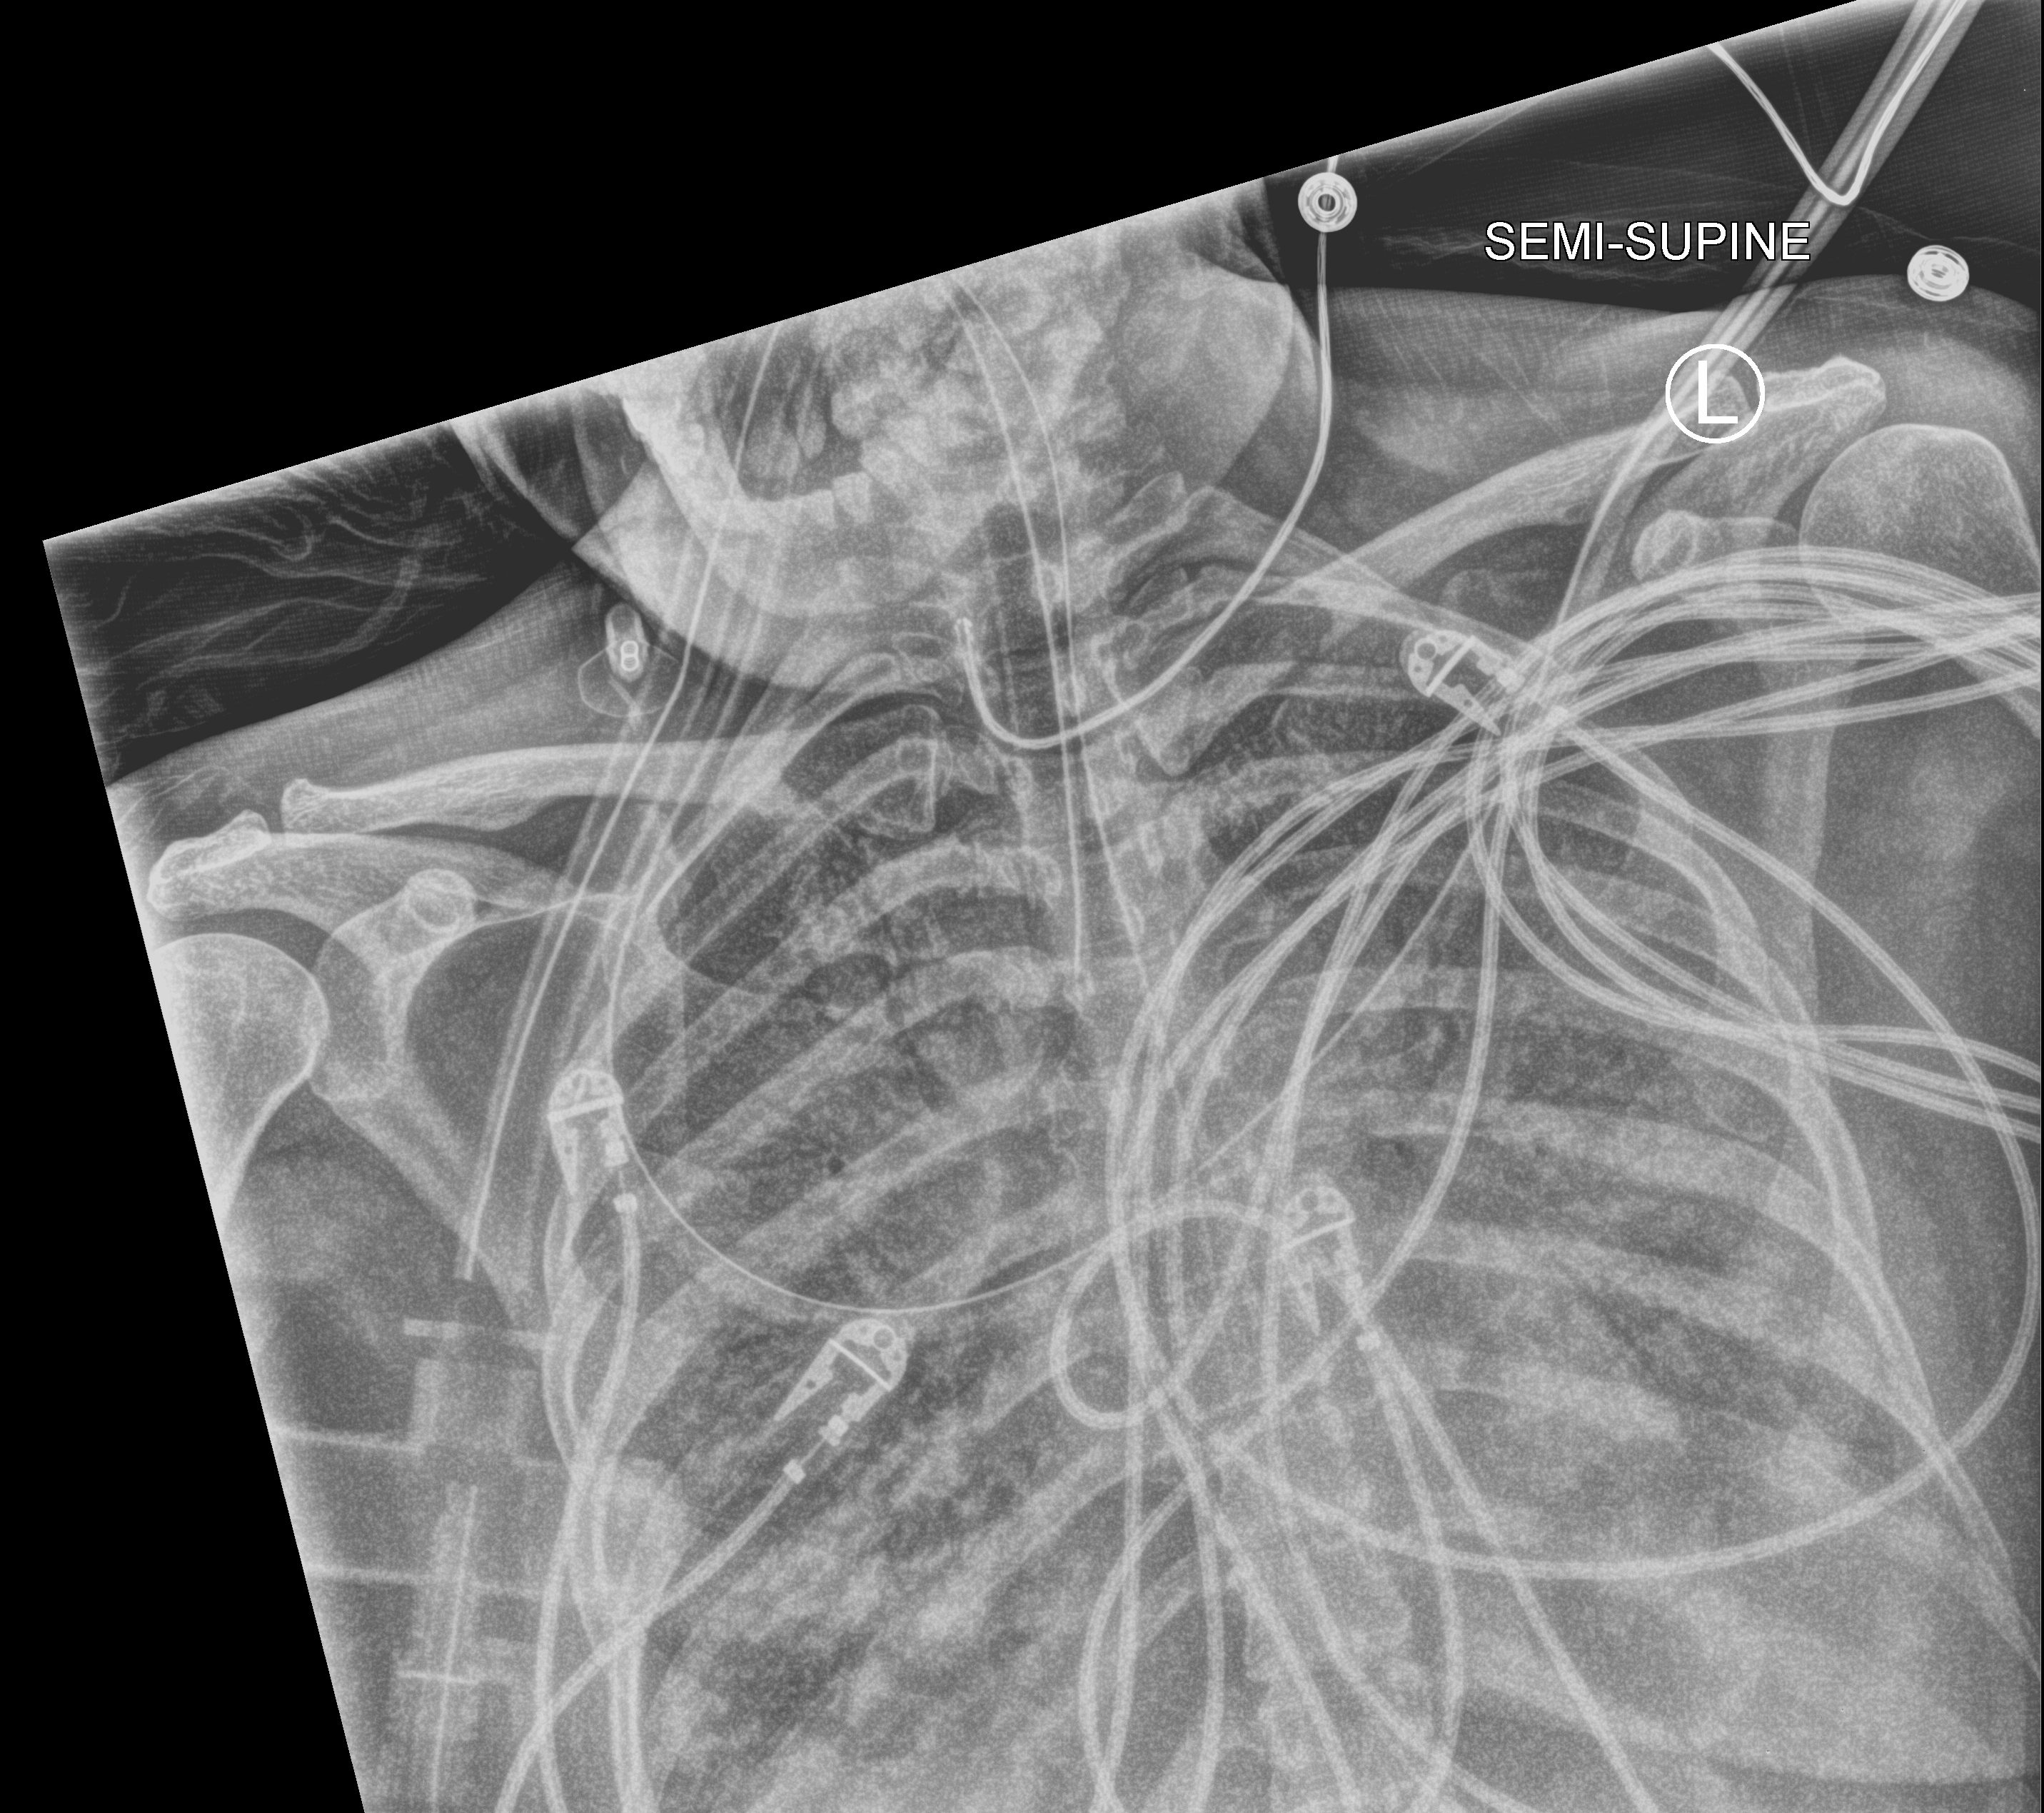
Chest X-ray (portable), anteroposterior (AP) projection. Male patient hospitalised with COVID-19, age 18–59 years.
Hospital-stay facts (about this admission, not read from this image; timing relative to this image not recorded): smoking status (admission record): never.